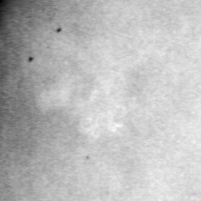
Crop from a digitized film mammogram around one marked abnormality, left breast, CC view.
Marked abnormality: calcifications, morphology pleomorphic, distribution clustered; BI-RADS assessment category 4; subtlety rating 2 on a 1 (subtle) to 5 (obvious) scale; pathology result (as recorded, not read from the image): benign.